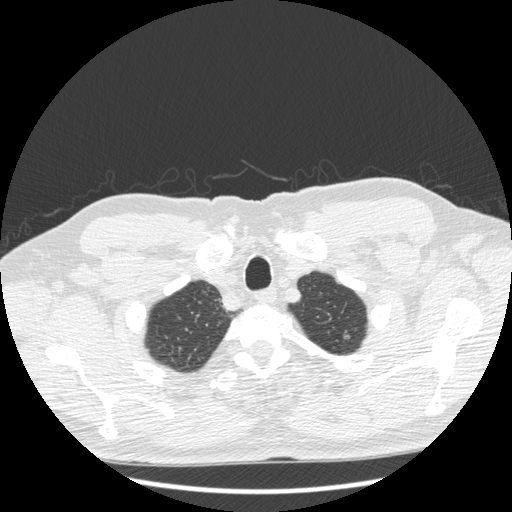
Axial slice from a low-dose chest CT screening exam; third annual screen; lung window (W 1500 / L -600 HU); standard (soft-tissue) reconstruction kernel (STANDARD); 512 × 512 image matrix, field of view 380 × 380 mm. Male, age 69 years at enrolment.
Lesion marked by an expert reader, bounding box <332,324,356,348> (left, top, right, bottom; pixels). The exam's reader record, not a measurement of the box and not confirmed to be the same lesion: non-calcified nodule or mass ≥4 mm, left upper lobe, 7 × 6 mm, smooth margins, soft tissue attenuation, pre-existing on the prior screen: yes; interval growth: yes. Later outcome: lung cancer diagnosed 112 days after this screen — adenocarcinoma, NOS, left upper lobe, moderately differentiated (G2), stage IA (AJCC 6th edition), 10 mm at pathology.